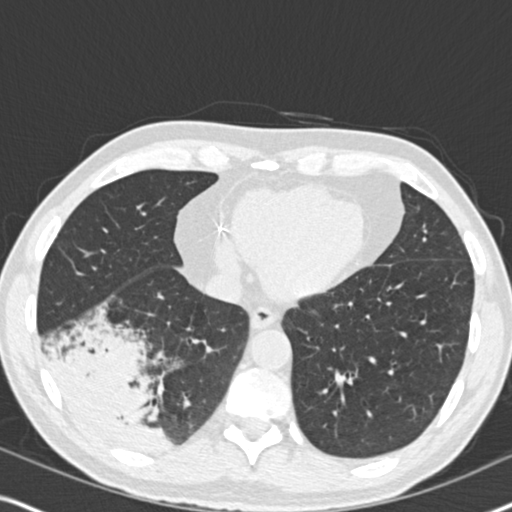
Low-dose screening chest CT, one axial slice; lung window (W 1500 / L -600 HU); 512 × 512 image matrix.
Annotated regions visible in this slice (expert manual segmentation):
- lesion 1 (tumor, lower lobe of right lung): bounding box (x1, y1, x2, y2) in pixels: (53, 326, 171, 454)